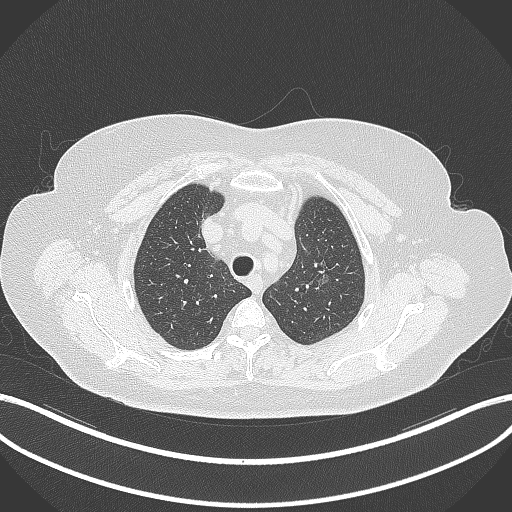
Chest CT, one axial slice; slice 274 of 309 in the series (ordered by position); reconstruction kernel B70f; lung window (W 1500 / L -600 HU); 1 mm slice thickness; 512 × 512 image matrix, field of view 400 × 400 mm. Female patient, age 70 years. Case-level facts recorded for this patient, not image findings: clinical TNM (as recorded): T1c N0 M0.
Outlined on this slice (rectangle marked by the reading radiologist):
- lung tumour (recorded histology: adenocarcinoma): bounding box <316,265,333,292> (left, top, right, bottom; pixels)